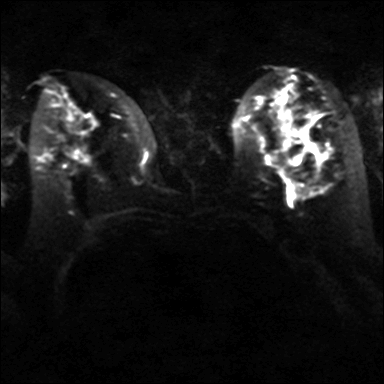
Breast MRI, one axial slice. Slice 18 of 40 in the series (ordered by position). Diffusion-weighted series; image 2 of 4 stored at this slice position (different b-values; order by instance number). 3 T. 4 mm slice thickness. 384 × 384 image matrix. Female patient.
Structures marked on this image (expert manual segmentation):
- tumour on diffusion-weighted imaging: bounding box [x1, y1, x2, y2] px = [289, 154, 300, 164]